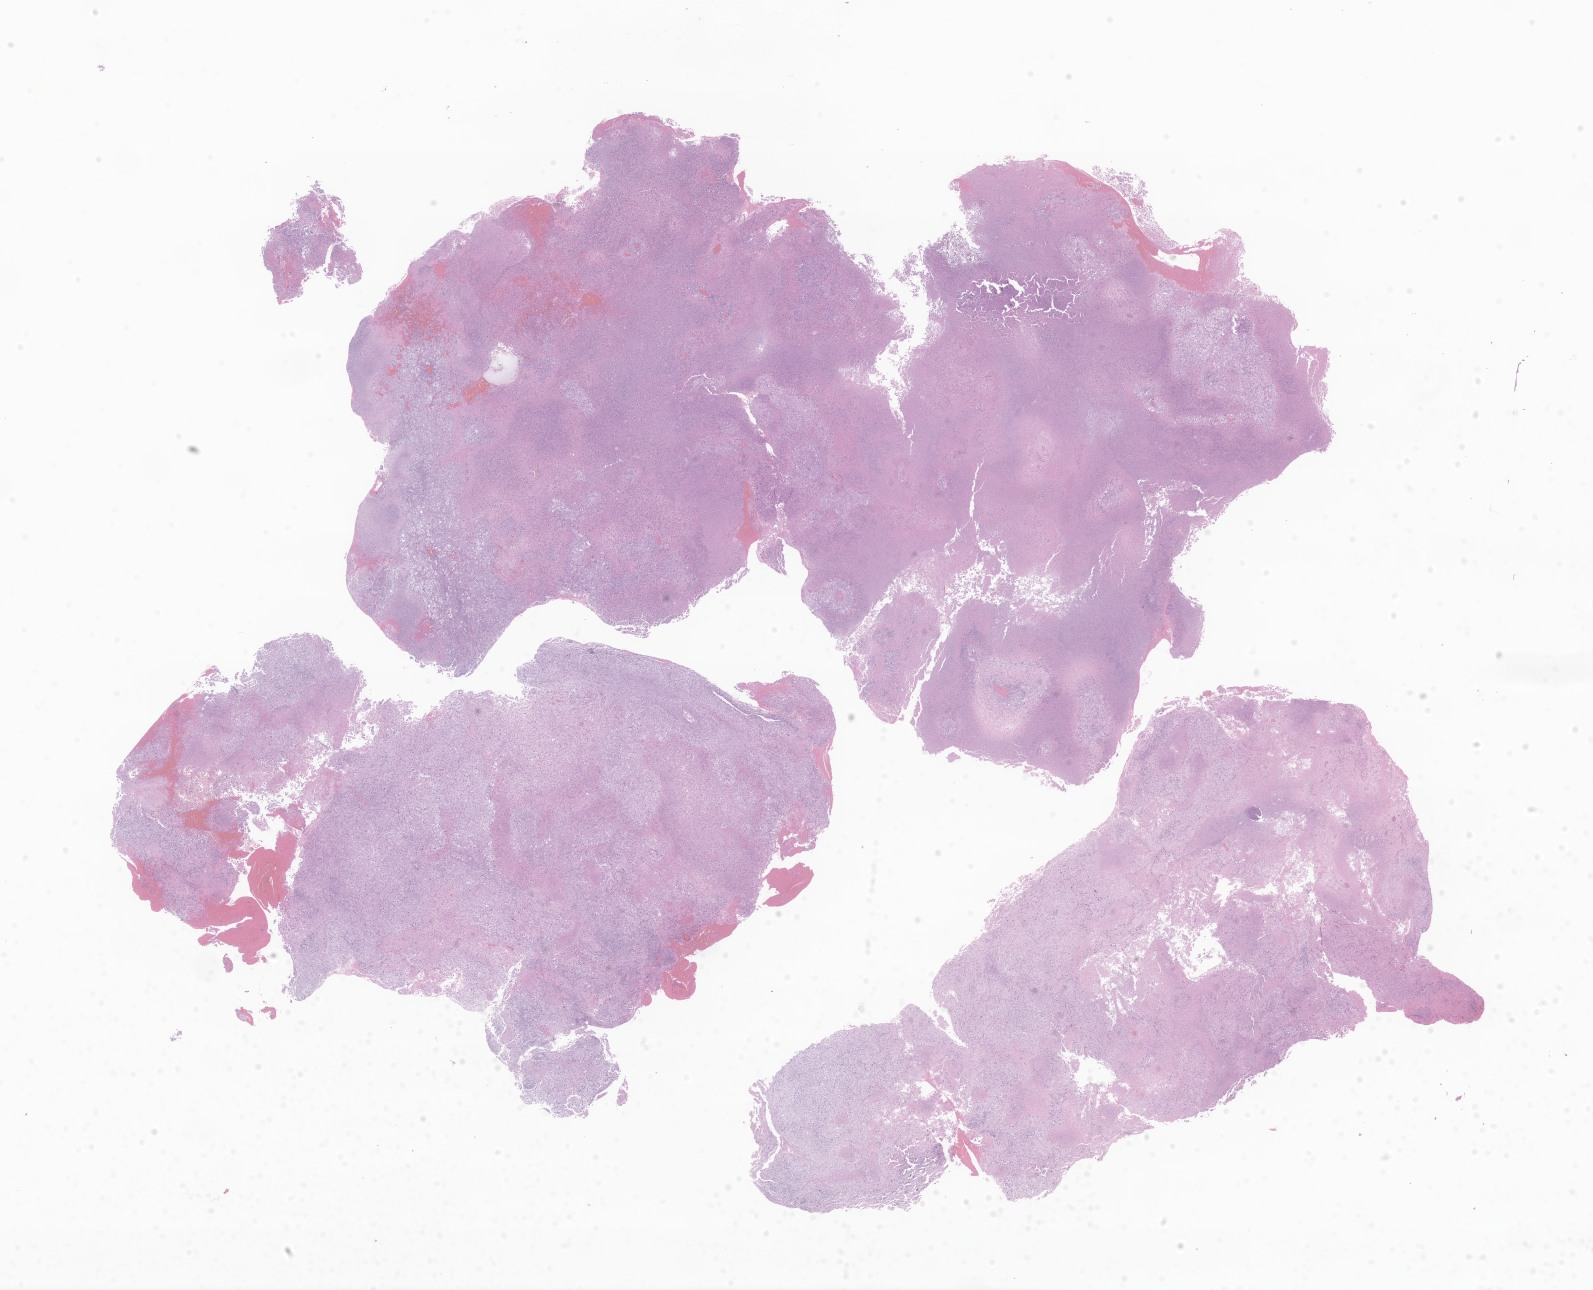
Hematoxylin and eosin (H&E) whole-slide image of tumor tissue from the brain — whole scanned area (about 26.9 x 21.8 mm) shown as a low-resolution overview; formalin-fixed, paraffin-embedded (FFPE) tissue. Patient male; age 47 months (3 years 11 months).
Recorded diagnosis: Neoplasm, uncertain whether benign or malignant.